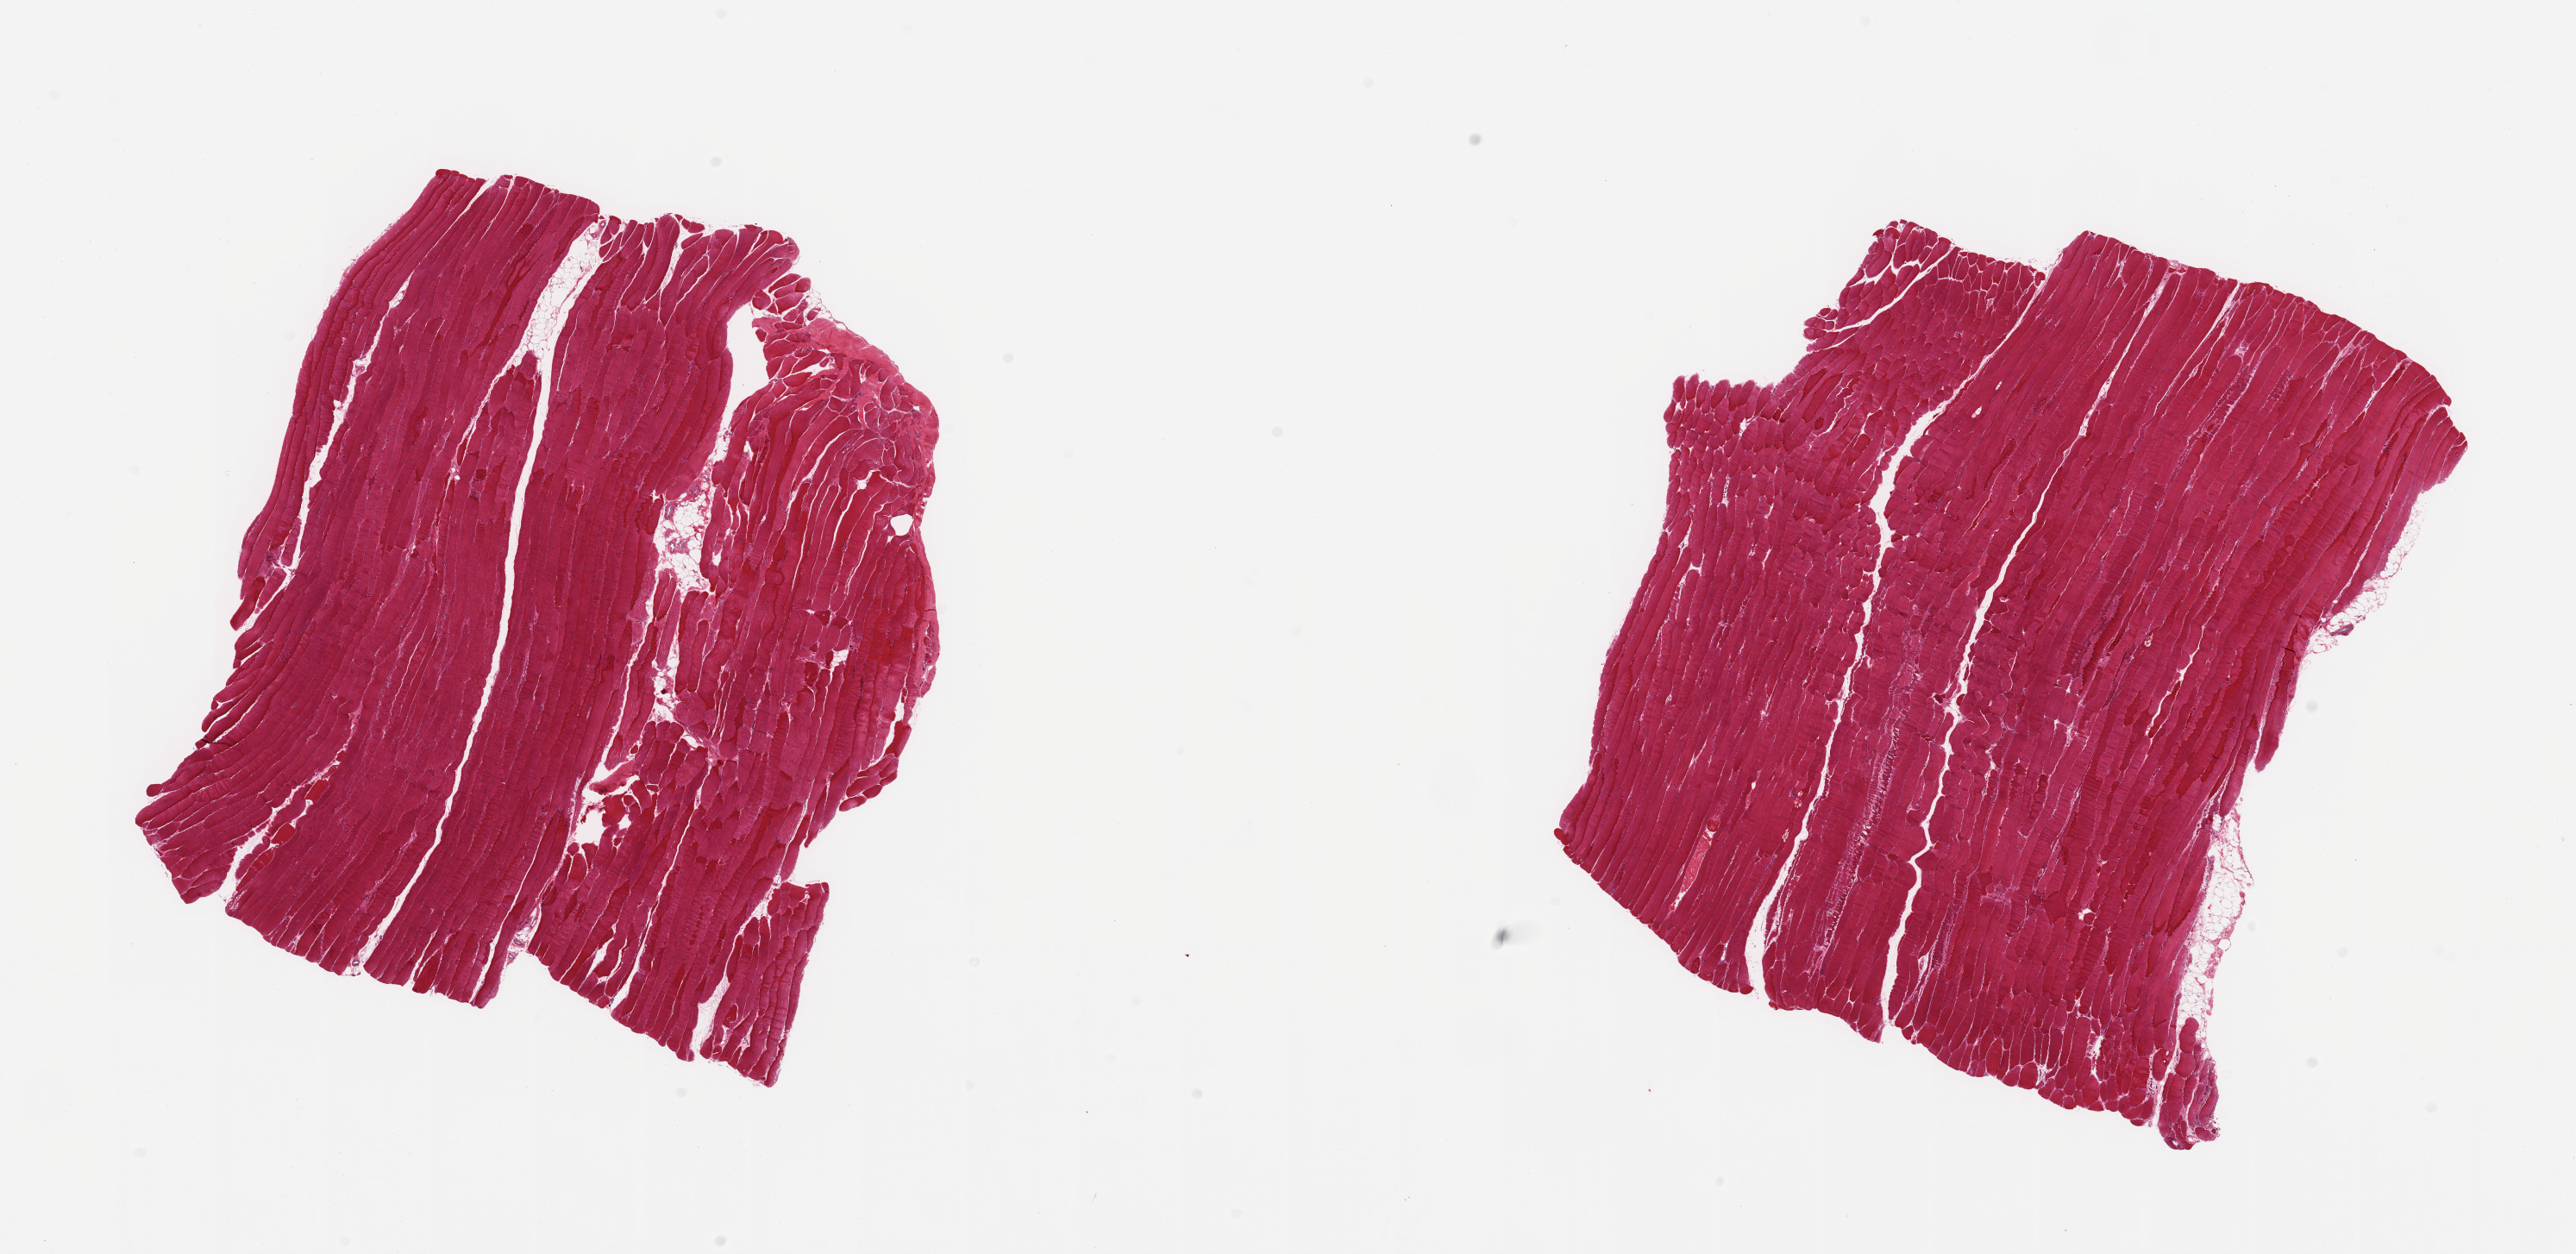
Hematoxylin and eosin (H&E) whole-slide image, brightfield — low-resolution overview of the scanned area, about 23.6 x 11.5 mm (acquisition: 20x scan); PAXgene-fixed, paraffin-embedded tissue; sampled site (target tissue): skeletal muscle; donor tissue sample. Donor: male.
Pathologist's review note for this sample: 2 pieces, <~10% interstitial fat.